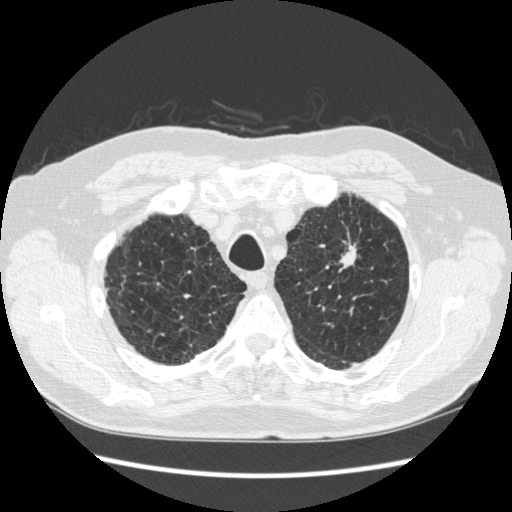
Low-dose screening chest CT, one axial slice. Slice 223 of 267 in the series (ordered by position). Lung window (W 1500 / L -600 HU). 512 × 512 image matrix, field of view 360 × 360 mm.
Outlined on this slice (manually delineated by an expert):
- lesion 1 (tumor, upper lobe of left lung): bounding box <340,246,356,267> (left, top, right, bottom; pixels)